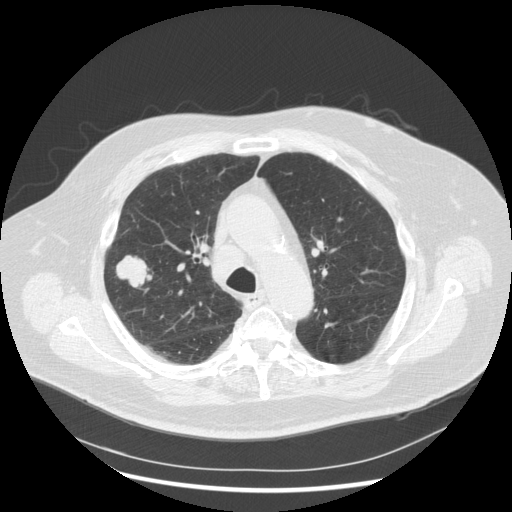
Chest CT (low-dose screening protocol), one axial image, third annual screen, lung window (W 1500 / L -600 HU), 2.5 mm slice thickness, standard (soft-tissue) reconstruction kernel (STANDARD), 120 kVp, slice 194 of 263 in the series, 512 × 512 image matrix. Male, age 72 years at enrolment. Former smoker at enrolment.
Expert reader's lesion annotation, bounding box (x1, y1, x2, y2) in pixels: (103, 250, 158, 299). The exam's reader record, not a measurement of the box and not confirmed to be the same lesion: non-calcified nodule or mass ≥4 mm, right upper lobe, 31 × 31 mm, poorly defined margins, soft tissue attenuation, pre-existing on the prior screen: no. Official screen result: positive, other. Participant outcome: lung cancer diagnosed 70 days after this screen — squamous cell carcinoma, NOS, right upper lobe, poorly differentiated (G3), stage IIIA (AJCC 6th edition), 19 mm at pathology.